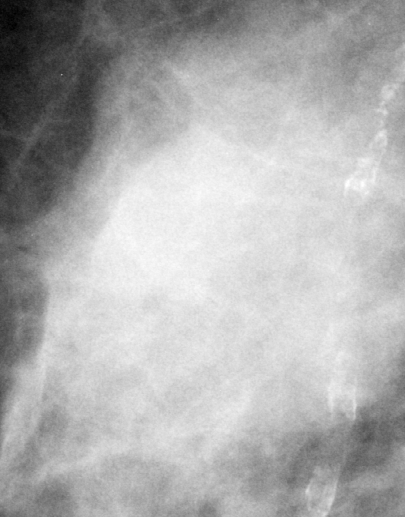
Region of interest cut from a scanned film mammogram (one marked finding), right breast, MLO view.
Mass, shape oval, margins ill defined; BI-RADS assessment category 5; subtlety rating 5 on a 1 (subtle) to 5 (obvious) scale; pathology (as recorded): malignant.